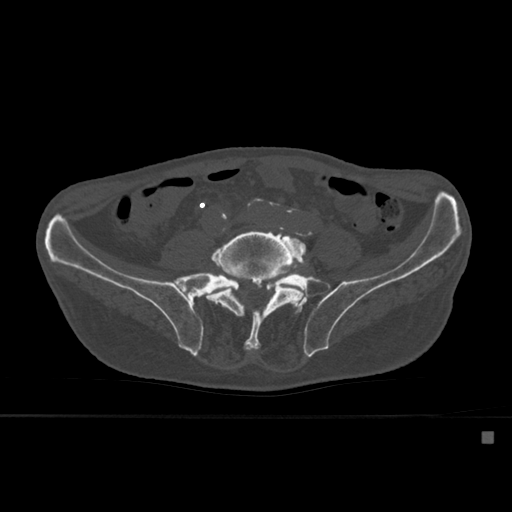
CT including the spine, one axial slice; slice 172 of 527 in the series (ordered by position); bone window (W 1800 / L 400 HU); 1.5 mm slice thickness; 512 × 512 image matrix. Male patient, age 78 years. Case-level facts recorded for this patient, not image findings: primary cancer: prostate.
Structures marked on this image (semi-automatic segmentation, software-assisted and operator-edited):
- L5 vertebra: bounding box [x1, y1, x2, y2] px = [206, 227, 307, 351]